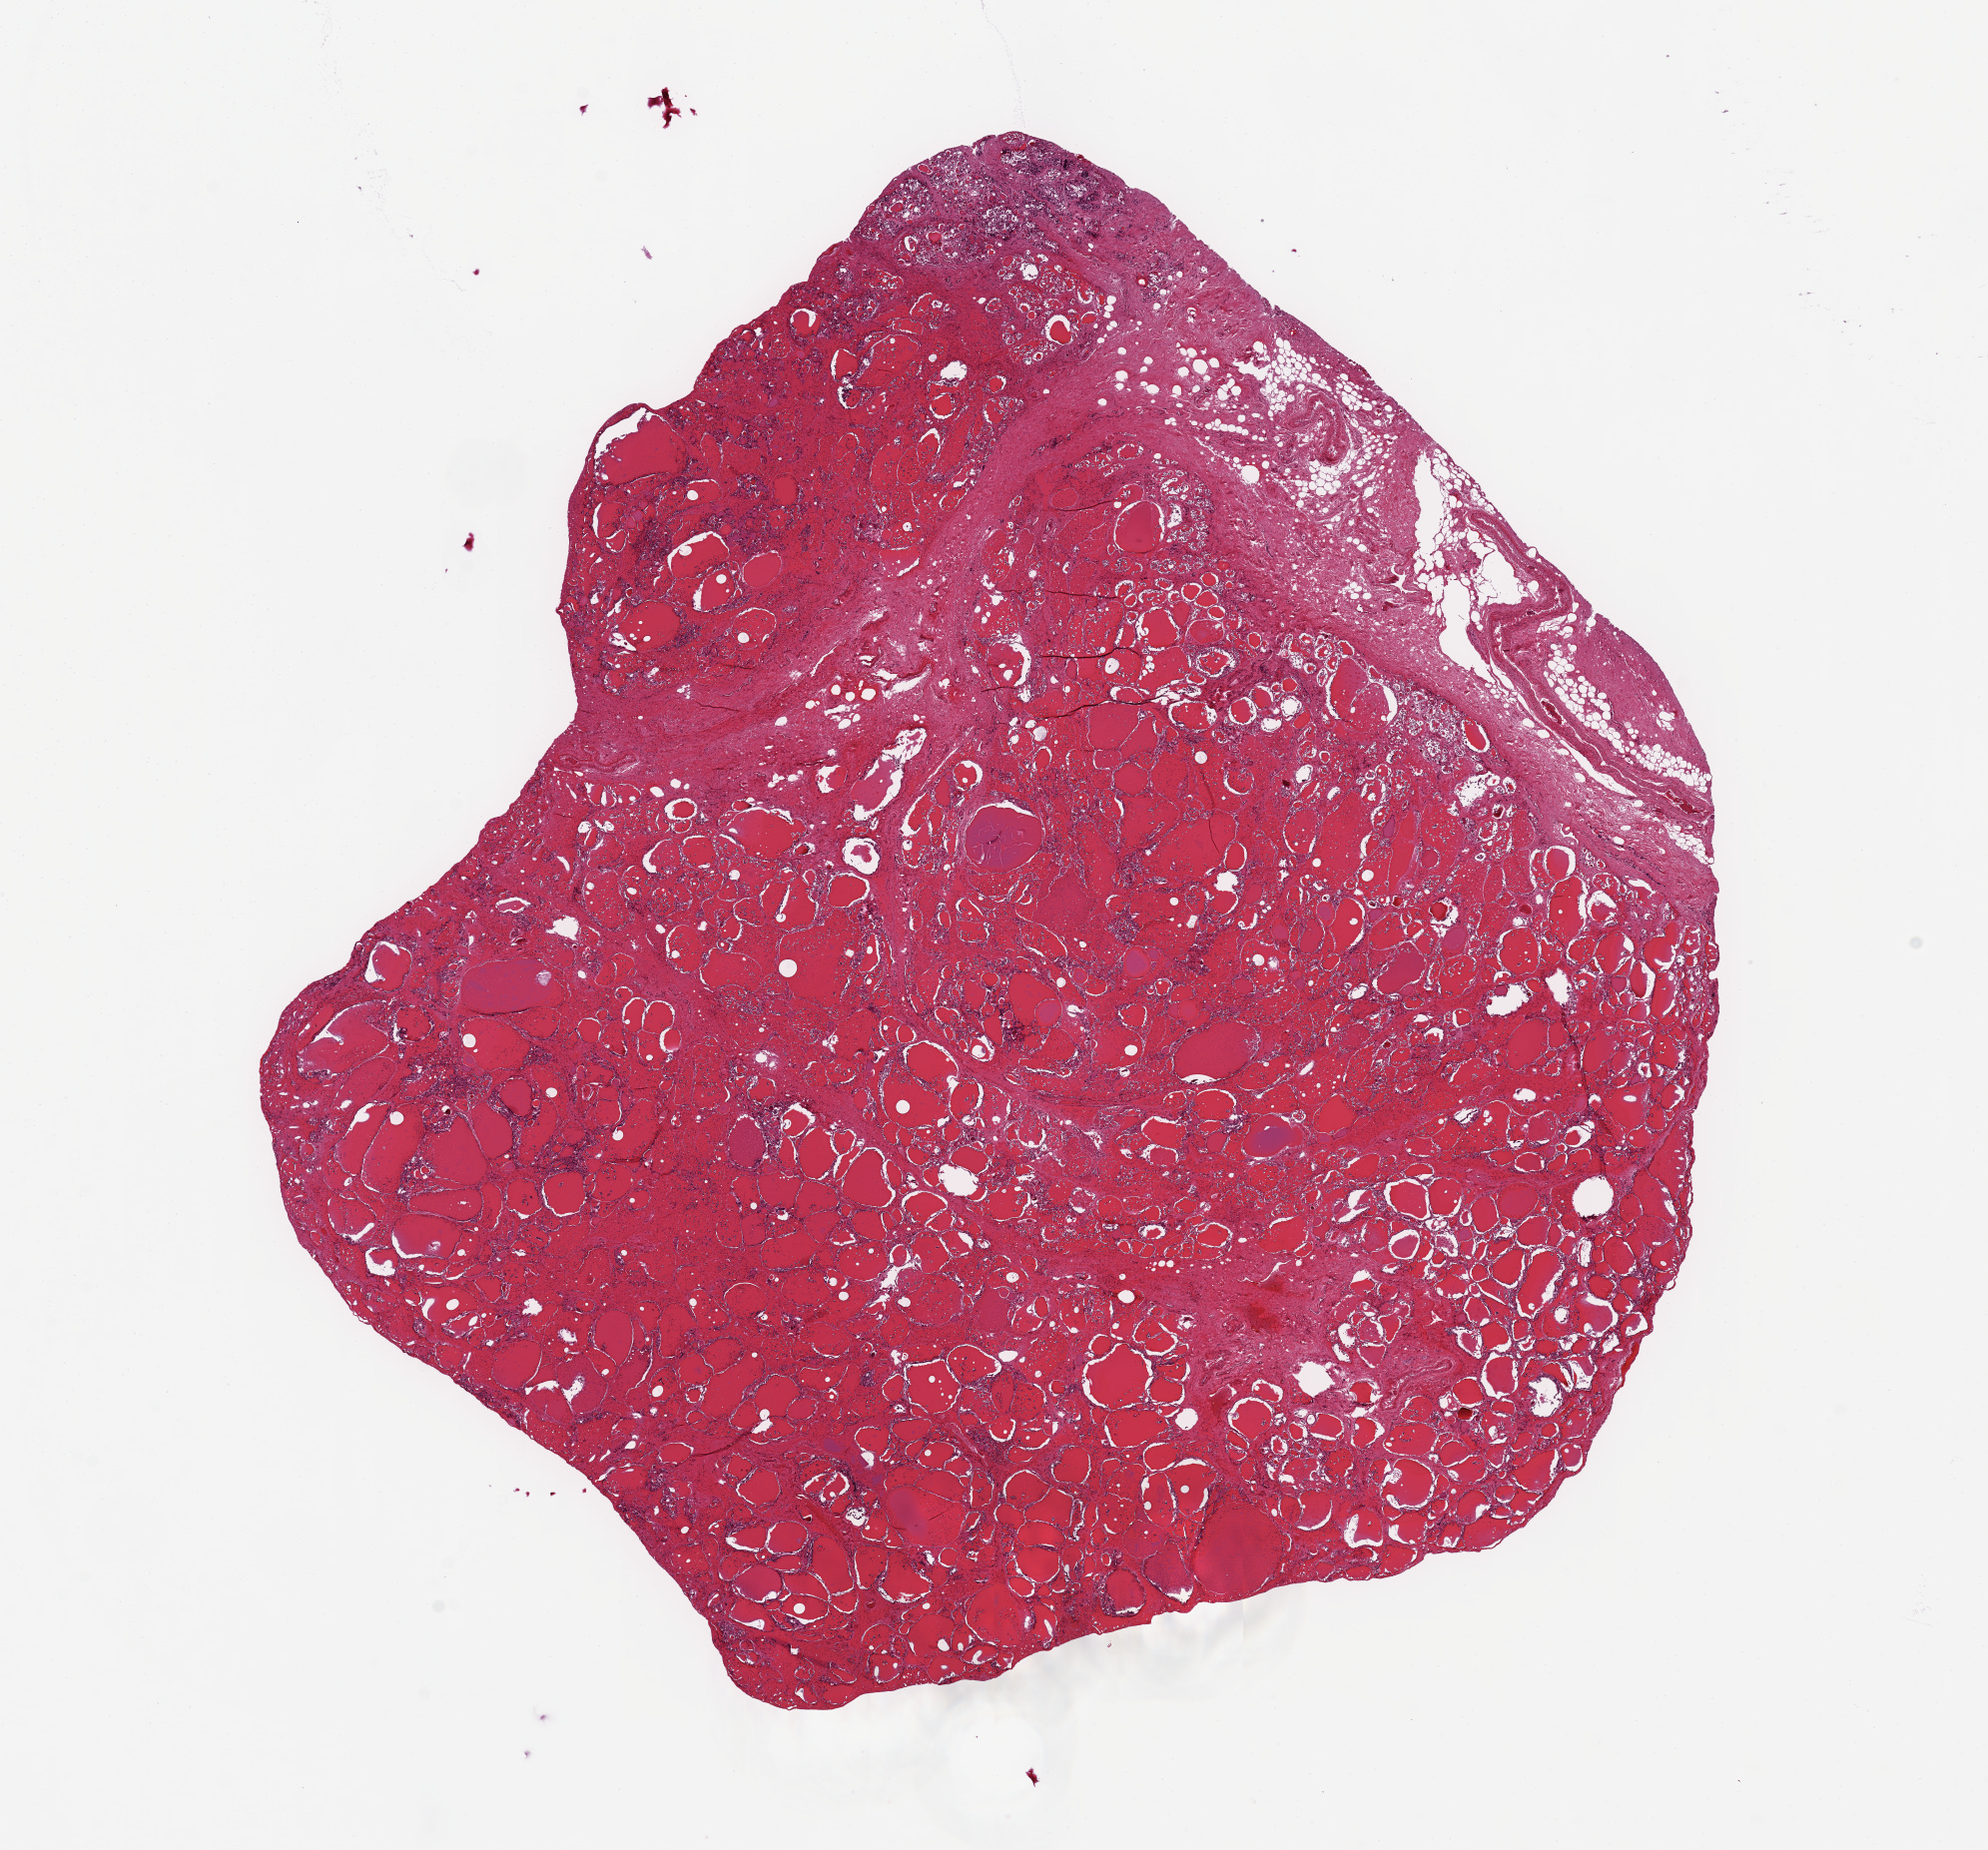
H&E whole-slide image — low-resolution overview of the scanned area, about 15.8 x 14.7 mm (slide scanned at 20x). PAXgene-fixed paraffin-embedded (PFPE) section. Section of thyroid (target tissue). Donor tissue sample. Donor: female.
Pathologist's review note for this sample: 12x12mm. Moderate fractures.